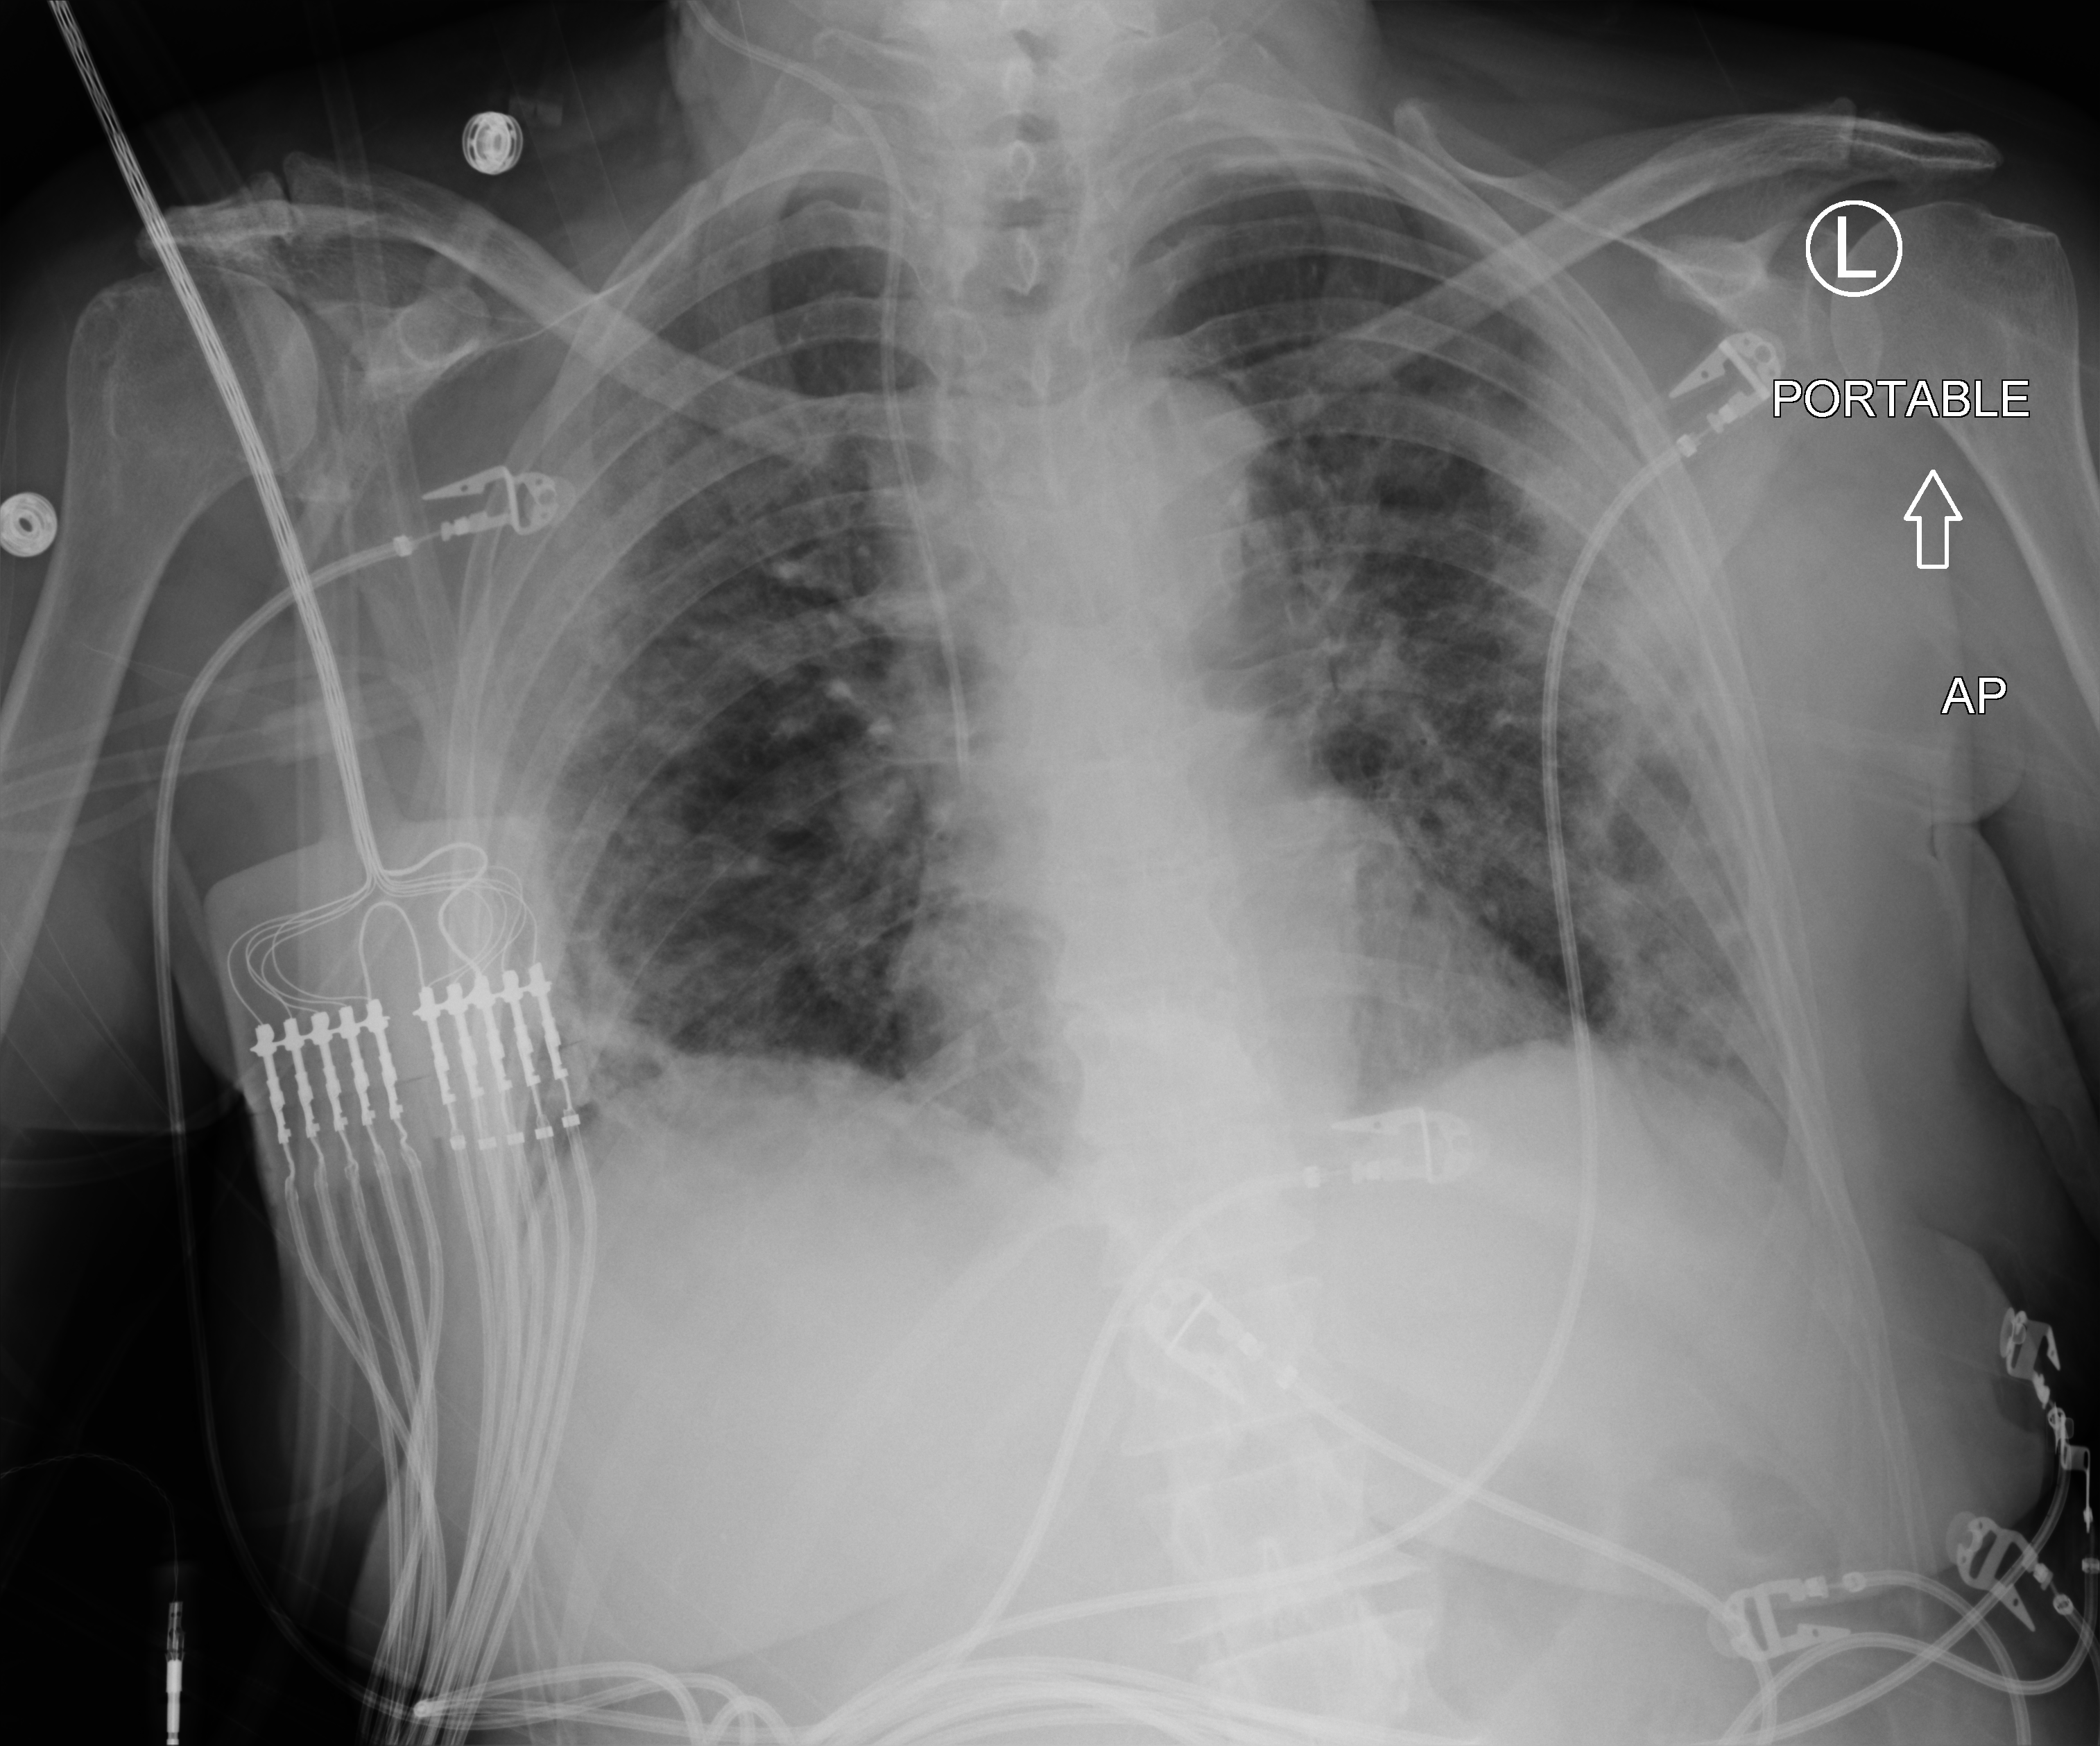
Portable chest radiograph; anteroposterior (AP) projection. Patient hospitalised with COVID-19; female, aged 60–74 years.
Admission-level facts for this patient (not findings on this image; timing relative to this image not recorded): admitted to intensive care during this hospital stay: yes.